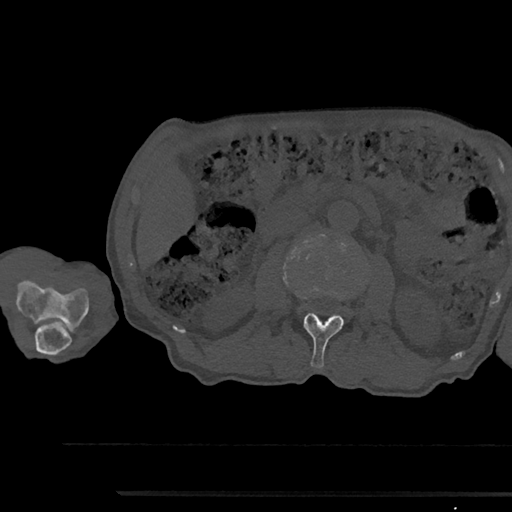
CT including the spine, one axial slice. Position 538 of 797 along the scan axis. Reconstruction kernel Br40s/3. 120 kVp. Bone window (W 1800 / L 400 HU). 0.5 mm slice thickness. 512 × 512 image matrix, field of view 367 × 367 mm. Male patient, age 79 years. Case-level facts recorded for this patient, not image findings: primary cancer: prostate.
Annotated regions visible in this slice (semi-automatic segmentation, software-assisted and operator-edited):
- L2 vertebra: box from (x=304, y=295) to (x=344, y=368) px